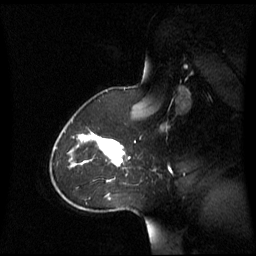
Breast MRI (dynamic contrast-enhanced), one sagittal slice; position 45 of 60 along the scan axis; dynamic contrast-enhanced series, image 2 of 3 at this slice position (ordered by acquisition); 1.5 T; TE 4.2 ms, TR 8.4 ms; 2.8 mm slice thickness; 256 × 256 image matrix, field of view 270 × 270 mm. Female patient, age 43 years. Case-level facts recorded for this patient, not image findings: setting: breast cancer imaged before/during neoadjuvant chemotherapy; receptor status: triple-negative.
Outlined on this slice (semi-automatically segmented with operator editing):
- analysis volume of interest (the breast-tissue region the enhancement analysis was run in; not a lesion): bounding box (x1, y1, x2, y2) in pixels: (62, 124, 127, 180)
- tumour enhancement mask (voxels above the 70 % enhancement threshold inside the analysis volume of interest): (78, 132, 125, 167)